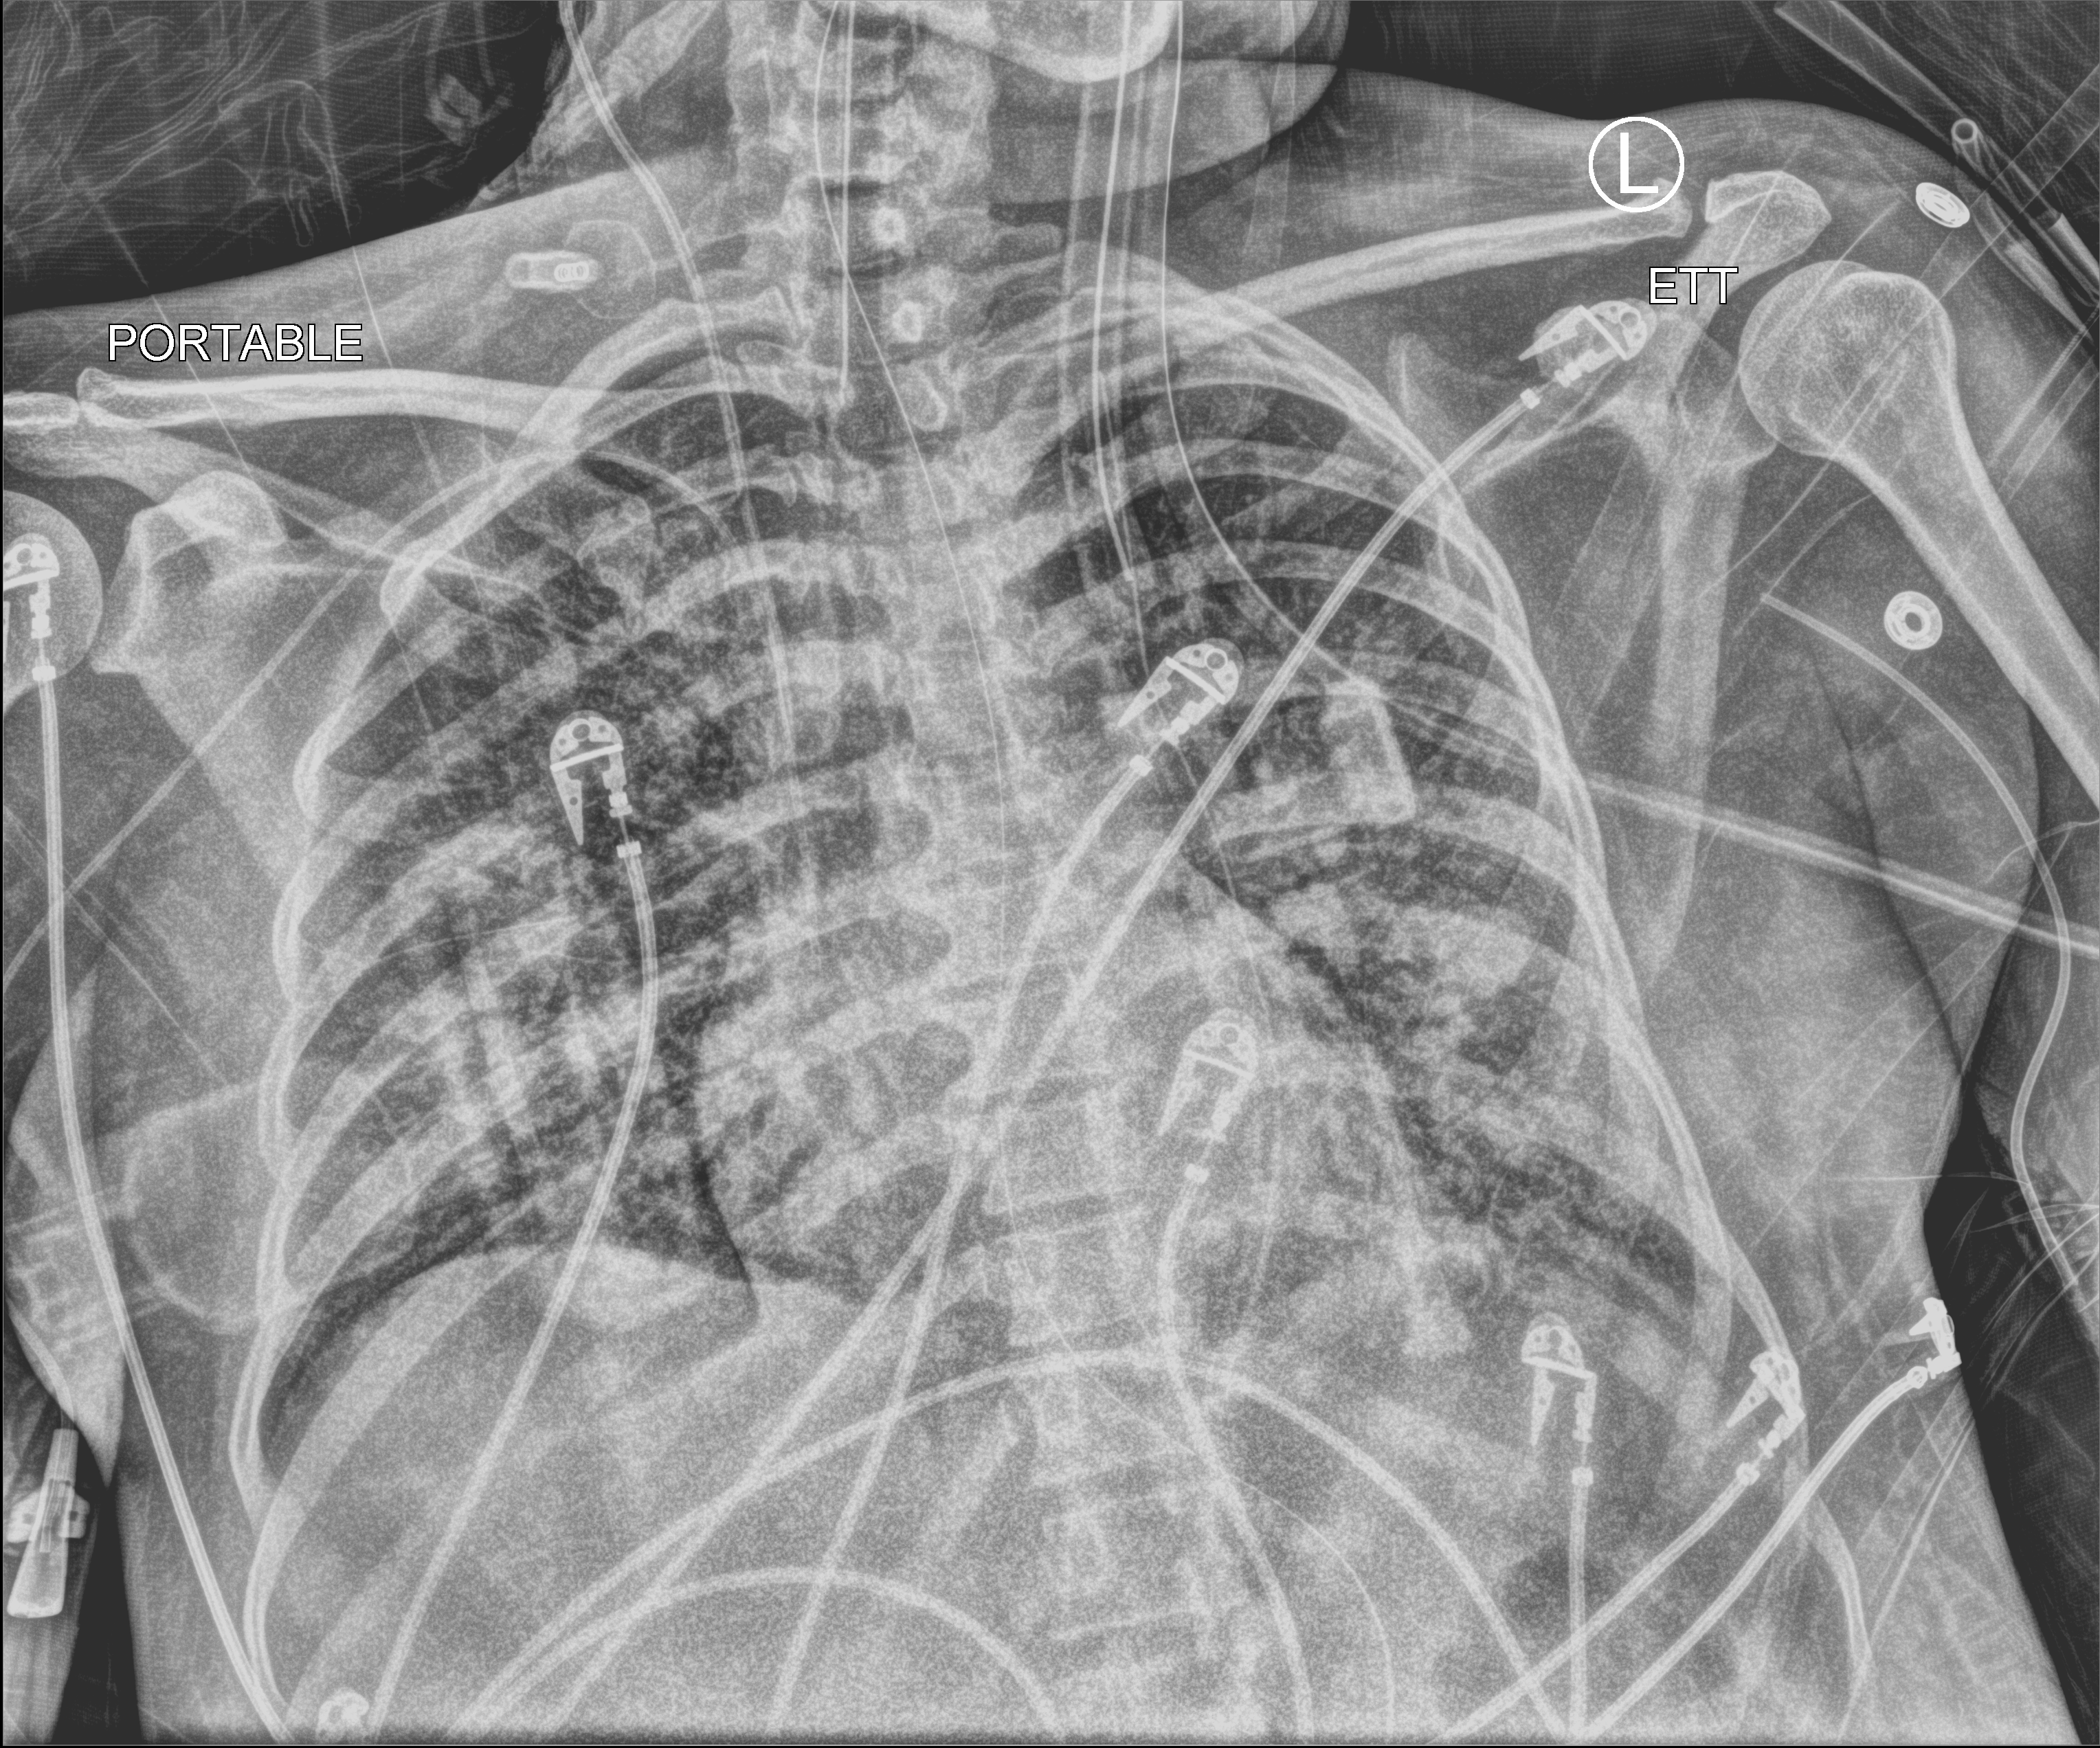
Portable chest radiograph. Female patient hospitalised with COVID-19, age 18–59 years.
Hospital-stay facts (about this admission, not read from this image; timing relative to this image not recorded): diabetes (admission record): no; mechanically ventilated during this hospital stay: yes; length of hospital stay: 71 days.